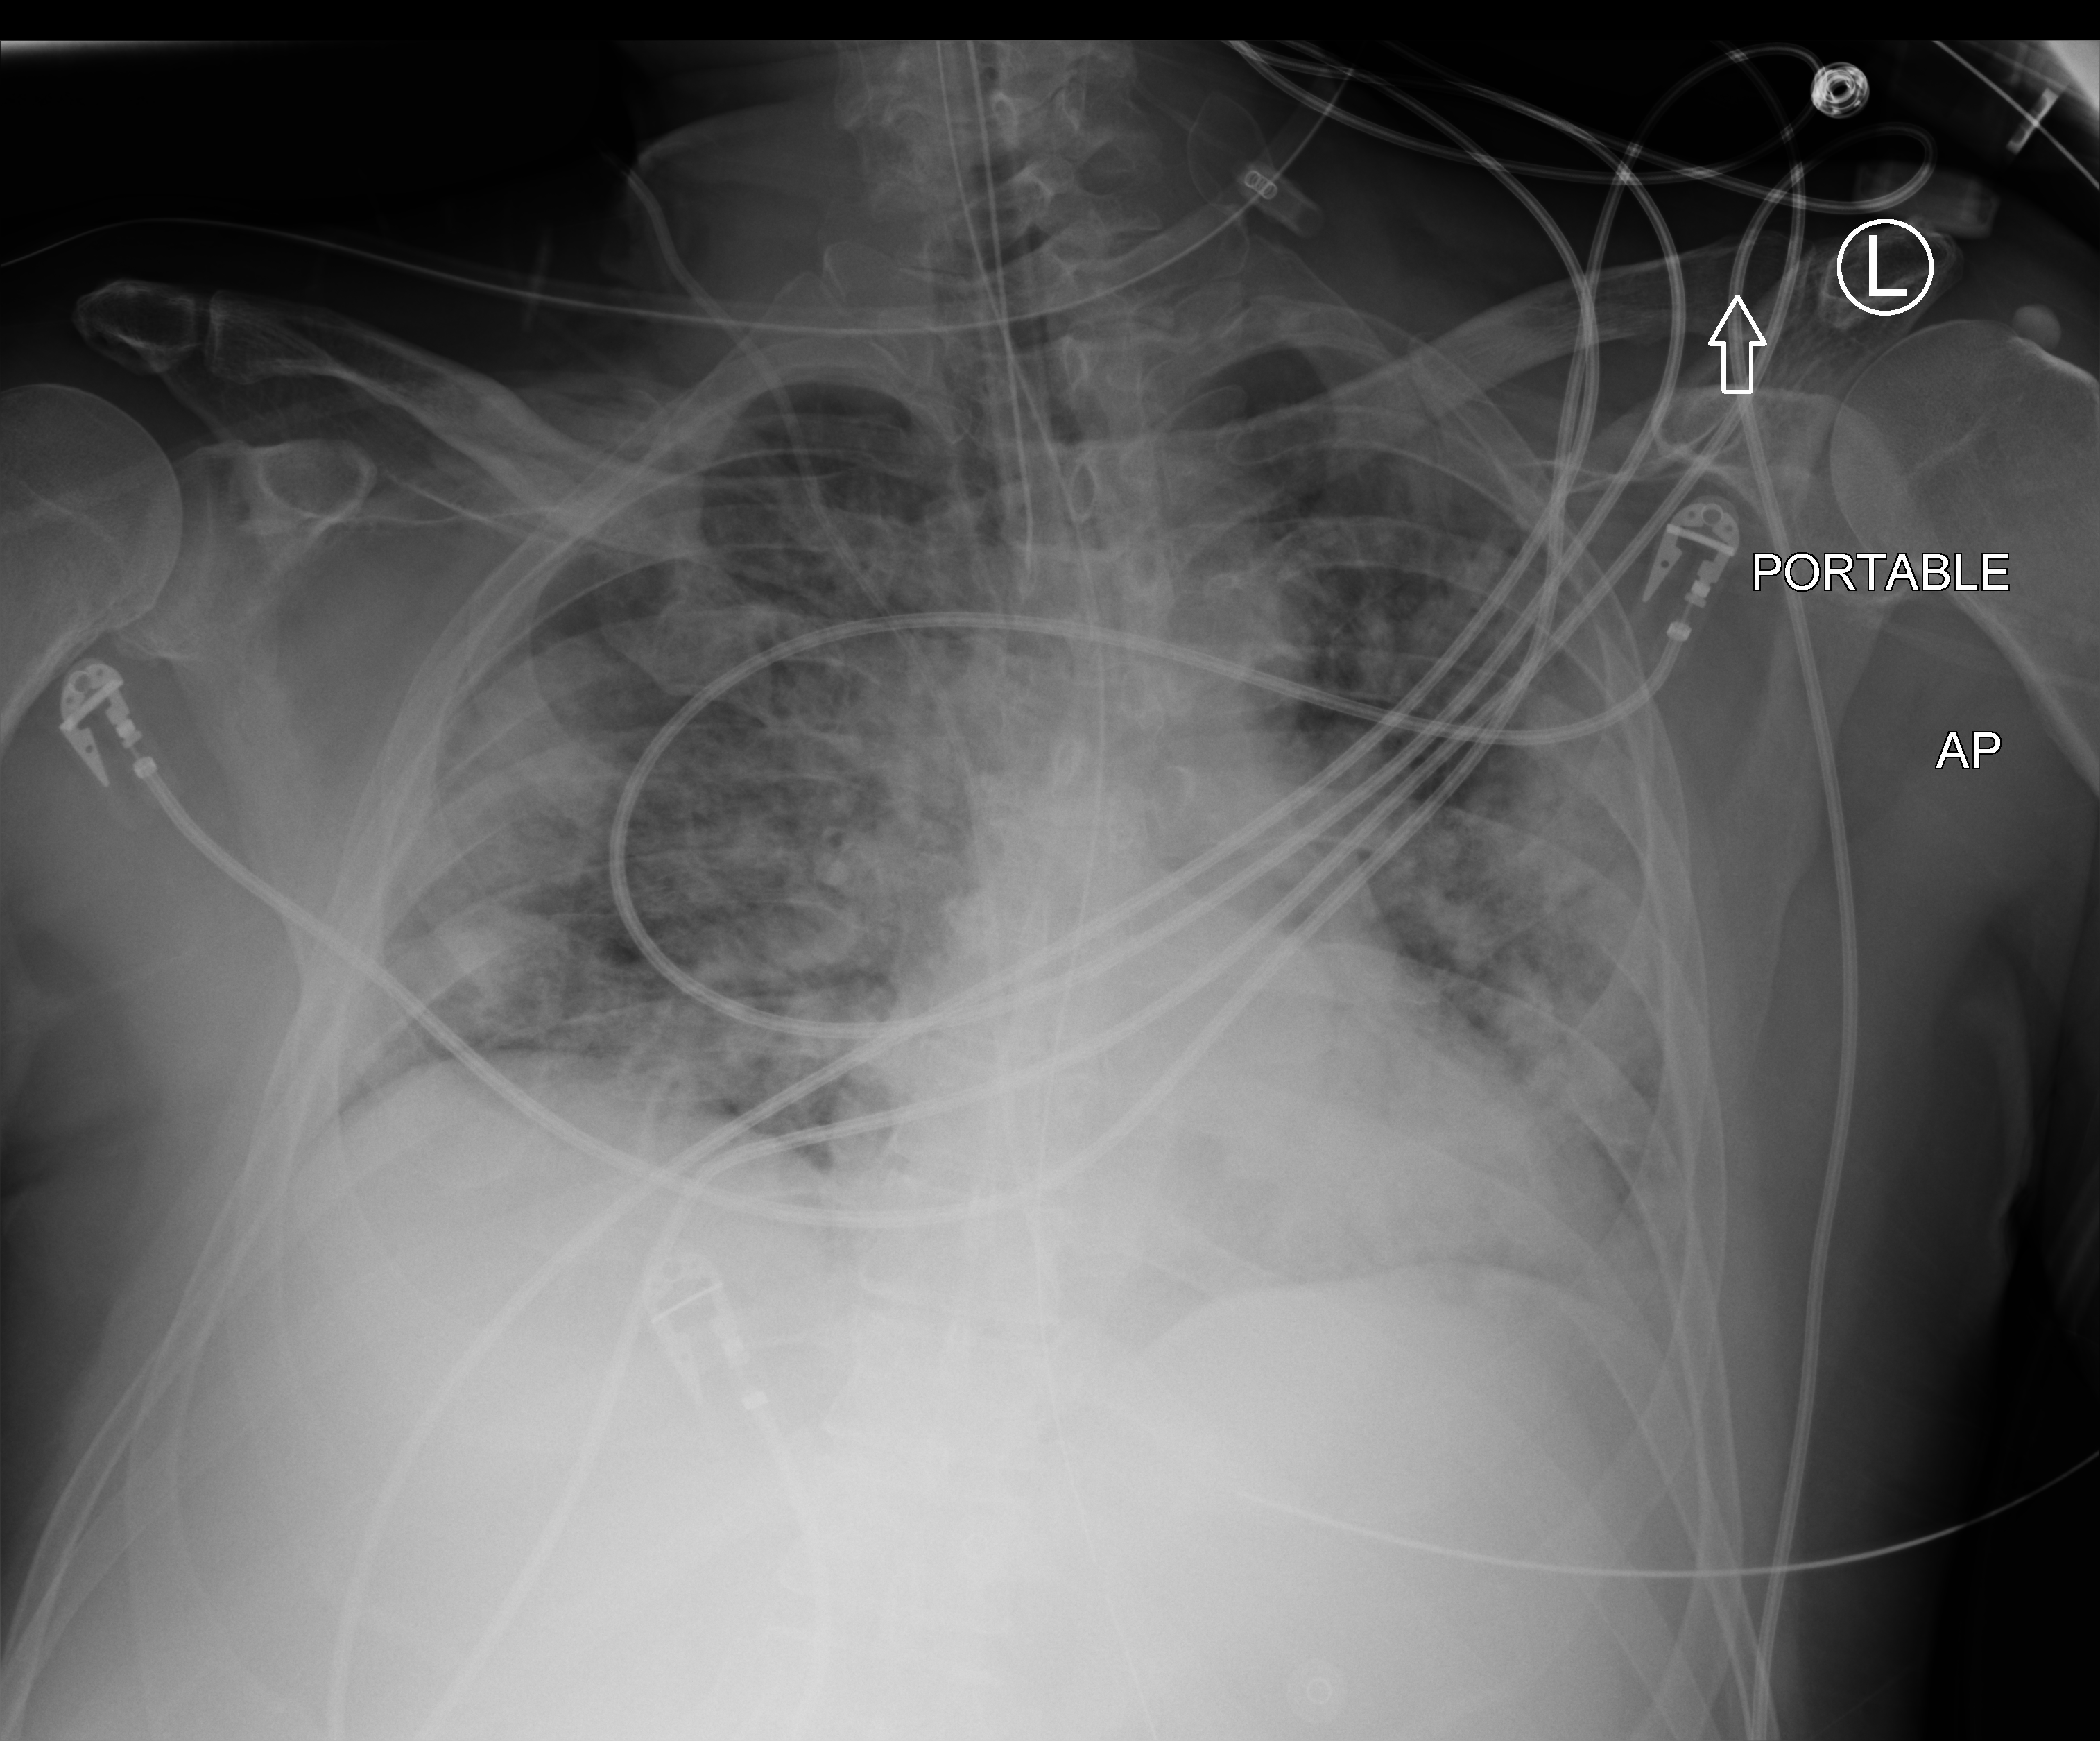
Chest X-ray (portable); anteroposterior (AP) projection. Patient hospitalised with COVID-19; male, aged 18–59 years.
From the hospital-stay record, not from the radiograph (when in the stay this image was taken is not recorded): mechanically ventilated during this hospital stay: yes; length of hospital stay: 25 days.